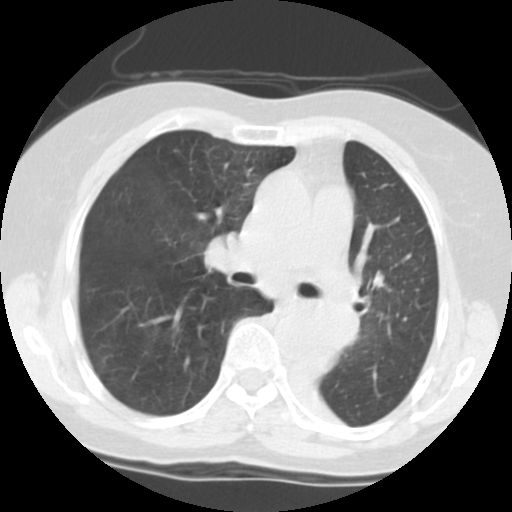
Low-dose screening chest CT, one axial slice. Slice 73 of 113 in the series (ordered by position). Reconstruction kernel STANDARD. Lung window (W 1500 / L -600 HU). 2.5 mm slice thickness. 512 × 512 image matrix, field of view 280 × 280 mm.
Structures marked on this image (outlined manually by an expert reader):
- lesion 1 (tumor, left main bronchus): box from (x=295, y=301) to (x=360, y=350) px